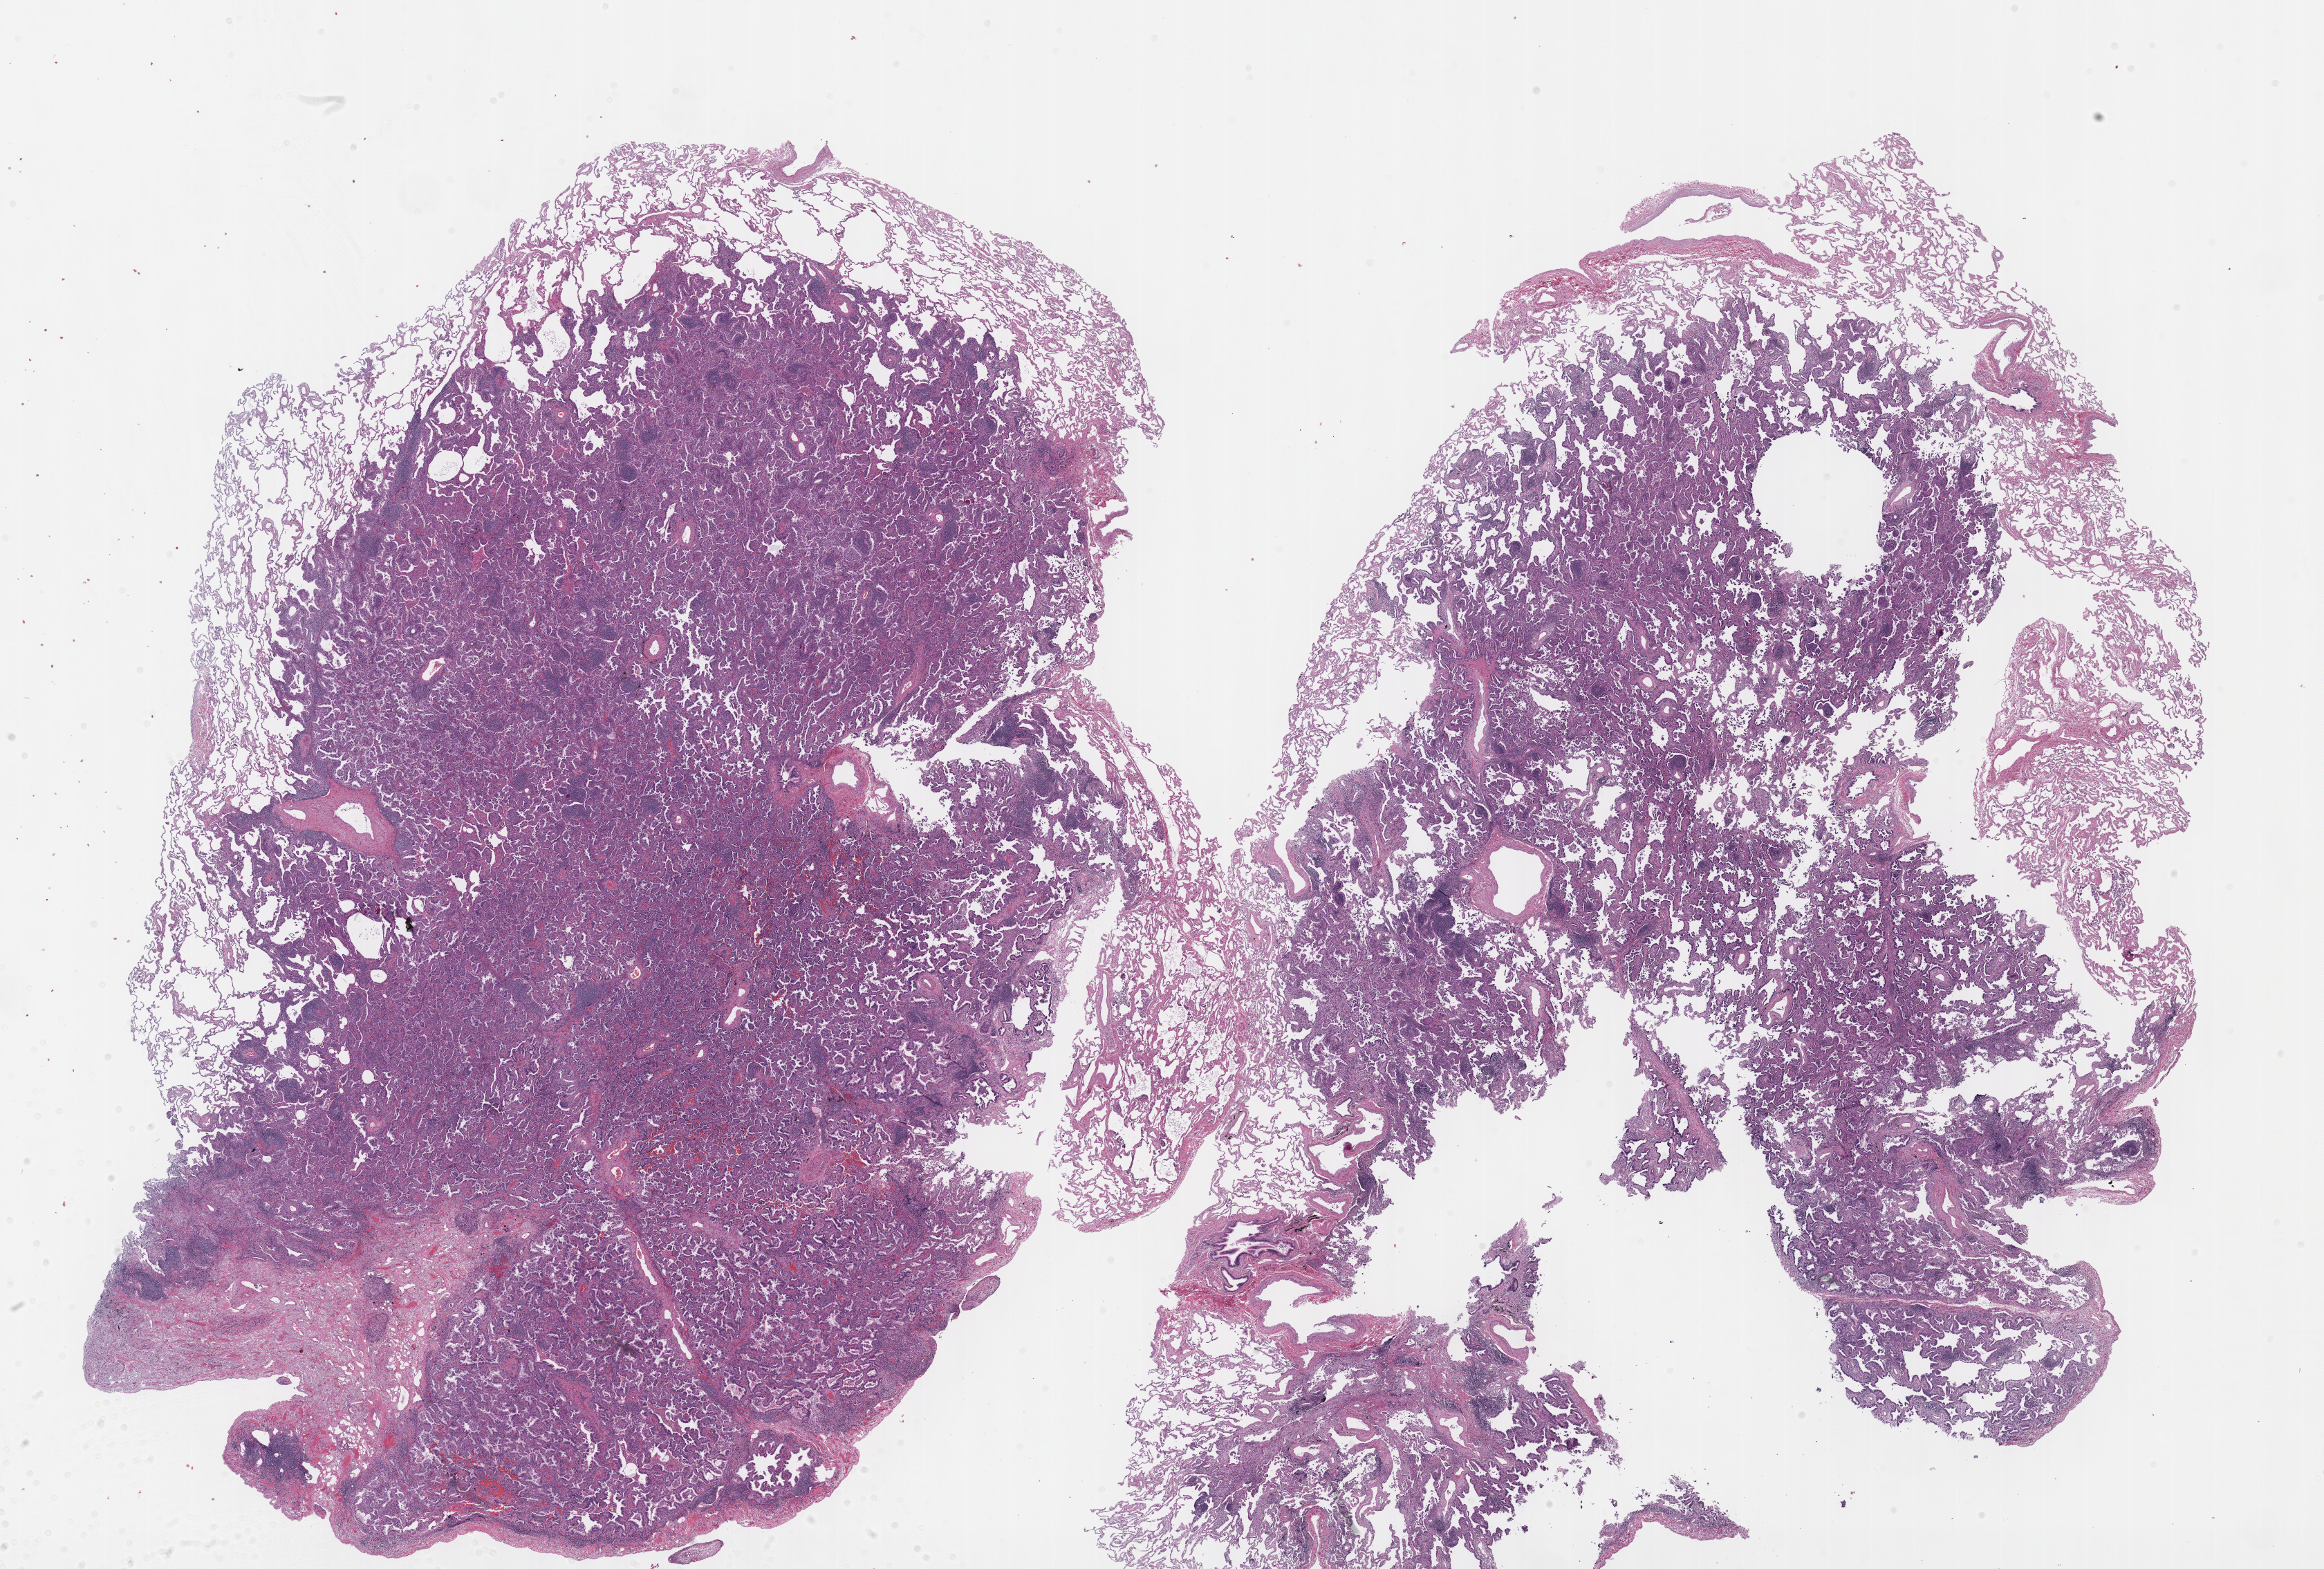
Digitized H&E tissue section (whole slide), whole scanned area (about 27.2 x 18.3 mm, from a 40x scan) shown as a low-resolution overview. Formalin-fixed paraffin-embedded (FFPE) diagnostic section. Lung, primary tumour sample. Female, age 70 years at initial diagnosis.
Histologic diagnosis: Adenocarcinoma, NOS (lower lobe, lung). Laterality: left. AJCC pathologic stage: IA (7th edition).